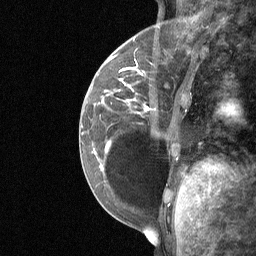
Breast MRI (dynamic contrast-enhanced), one sagittal slice. Dynamic contrast-enhanced study with each time point stored as its own series, time point 2 of 3 at this slice position (early post-contrast, ordered by acquisition time). 1.5 T. TE 4.8 ms, TR 27 ms. 256 × 256 image matrix, field of view 200 × 200 mm. Patient: female, 34 years. Case-level facts recorded for this patient, not image findings: setting: breast cancer imaged before/during neoadjuvant chemotherapy; receptor status: HR-positive, HER2-negative.
Annotated regions visible in this slice (semi-automatically segmented with operator editing):
- analysis volume of interest (the breast-tissue region the enhancement analysis was run in; not a lesion): bounding box [x1, y1, x2, y2] px = [92, 50, 188, 185]
- tumour enhancement mask (voxels above the 90 % enhancement threshold inside the analysis volume of interest): [119, 68, 149, 110]